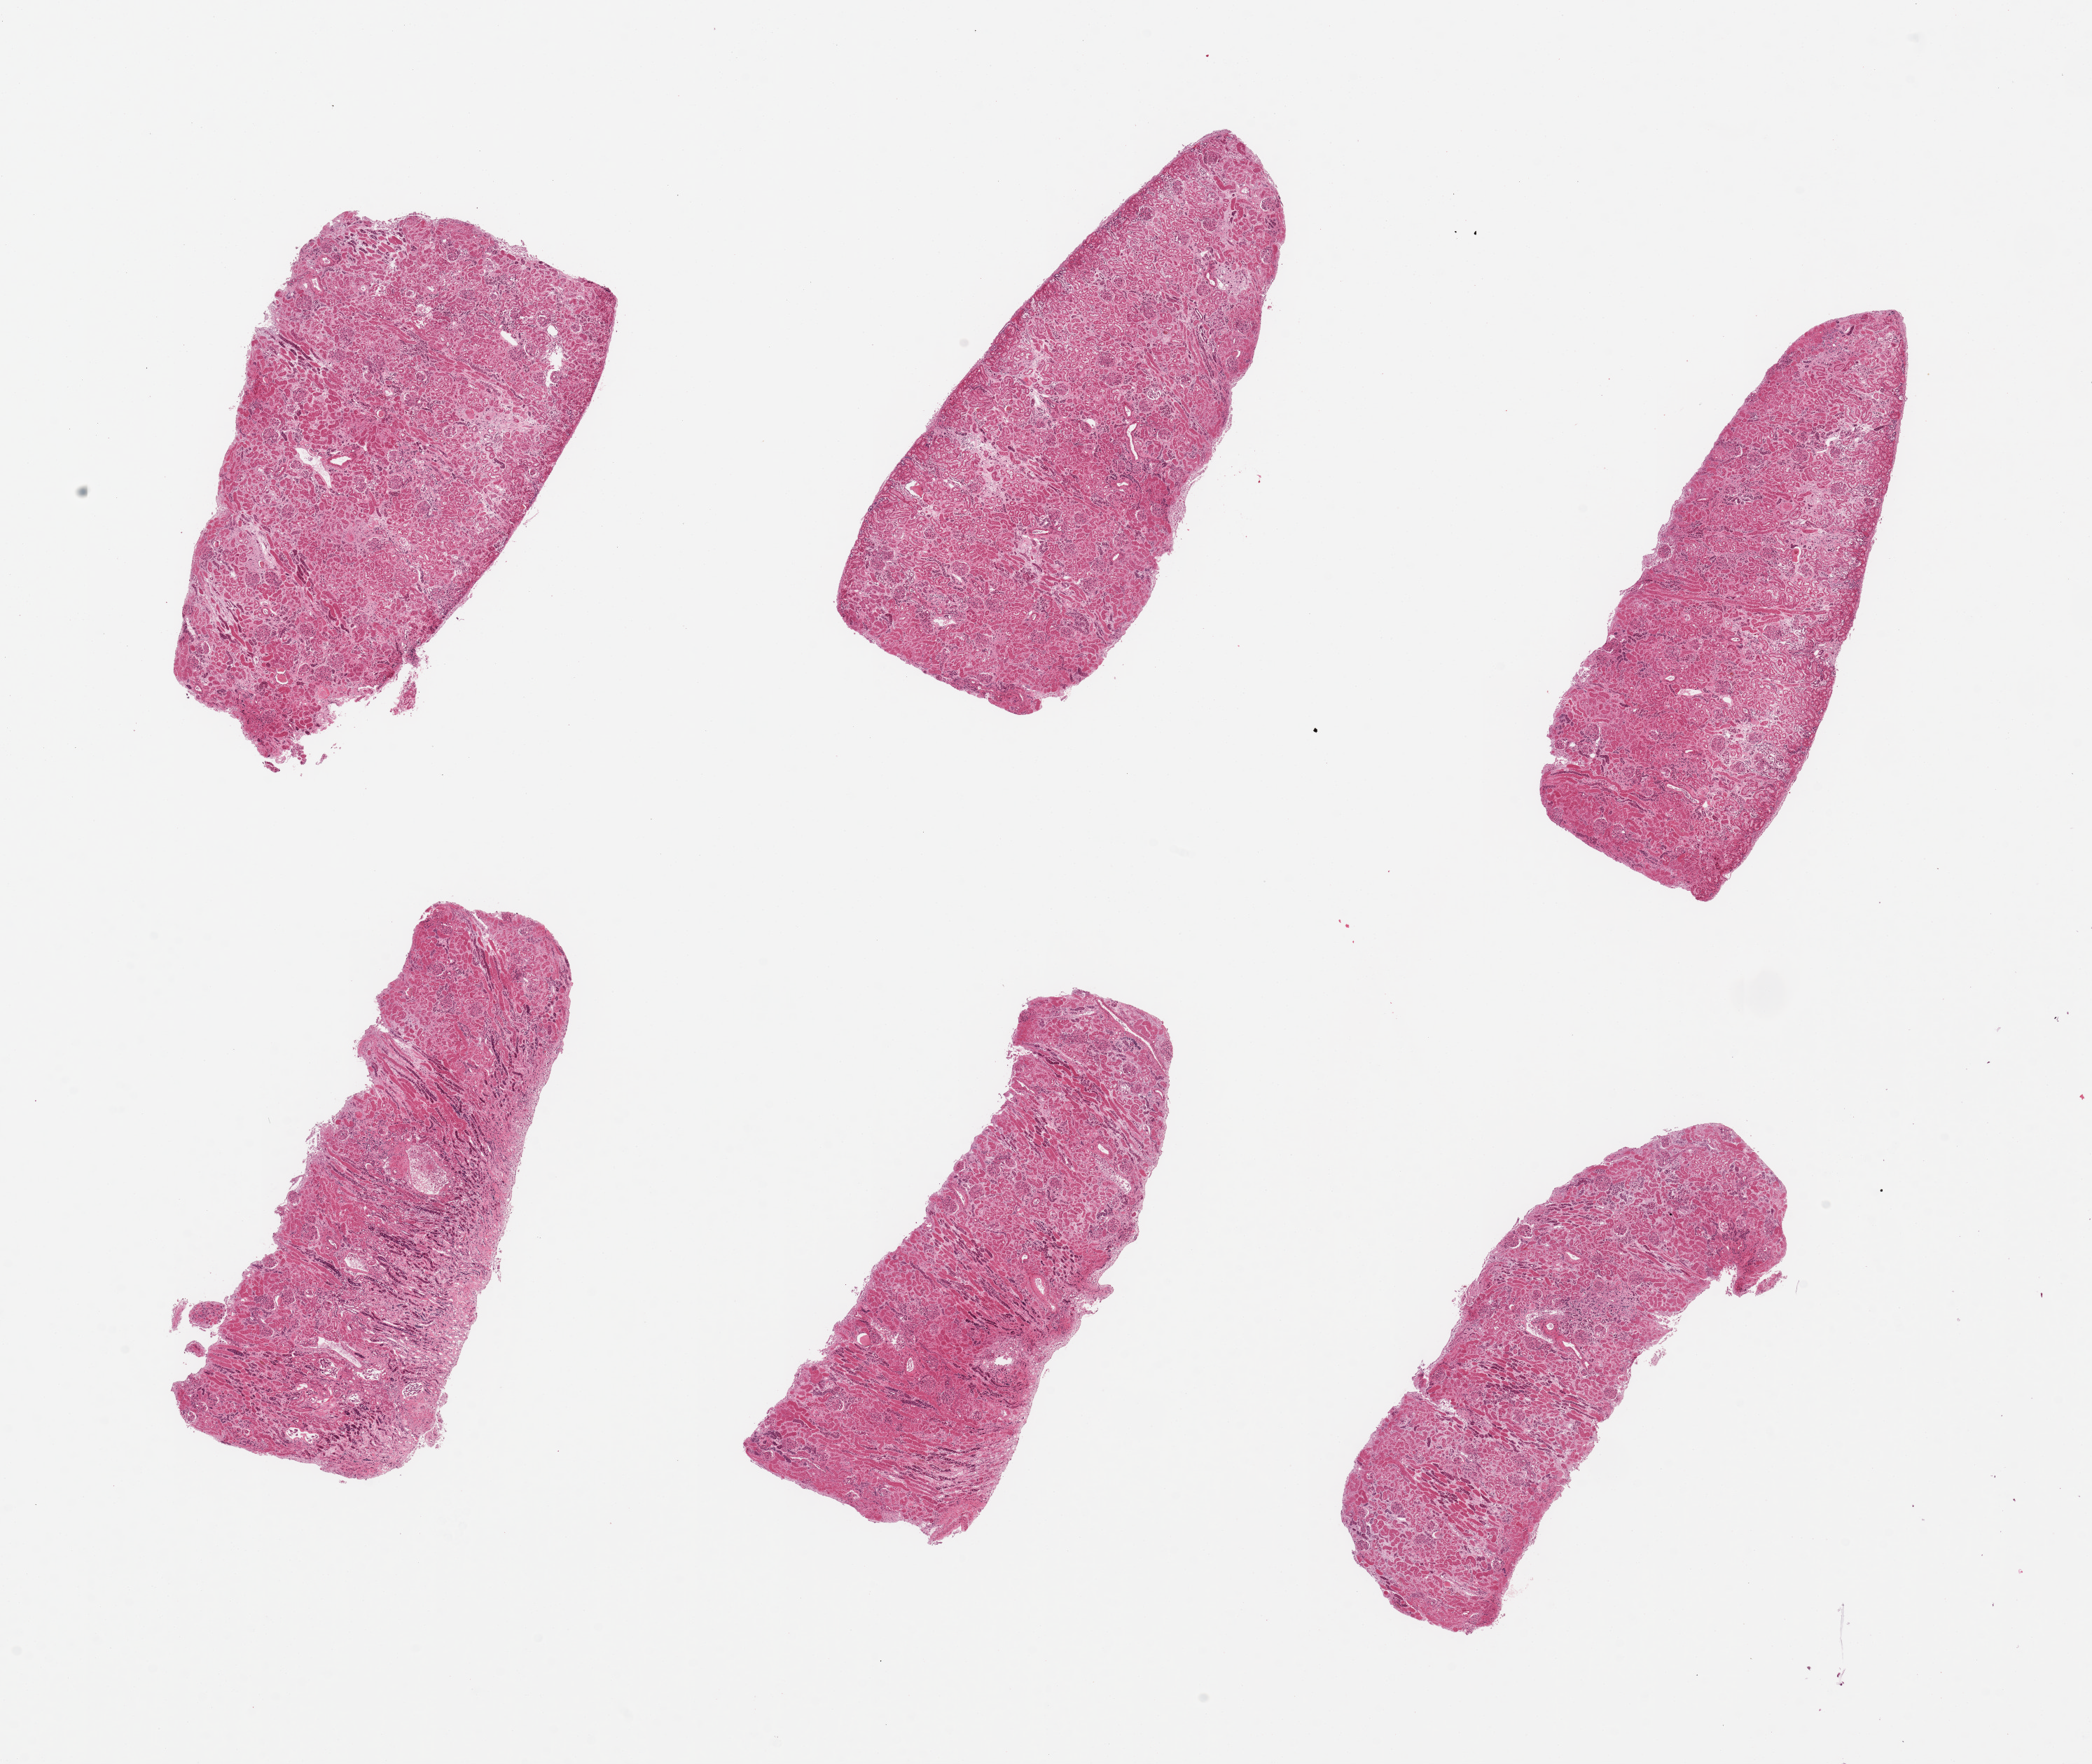
Whole-slide image, hematoxylin and eosin (H&E) stain, whole scanned area (about 23.6 x 19.9 mm) shown as a low-resolution overview; PAXgene-fixed paraffin-embedded (PFPE) section; section of renal cortex (target tissue); tissue donor sample. Male donor.
Reviewer comment on this tissue sample: 6 pieces, up to 7x3mm;scattered fibrosed glomeruli.